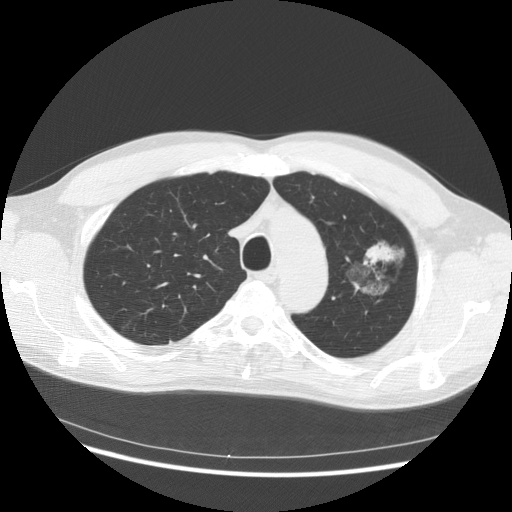
Axial slice from a low-dose chest CT screening exam, third screening round (two years after baseline), lung window (W 1500 / L -600 HU), 2.5 mm slice thickness, slice 109 of 145 in the series, 512 × 512 image matrix. Male, age 61 years at enrolment.
• Lesion marked by an expert reader, box from (x=331, y=236) to (x=406, y=316) px.
• The exam's reader record, not a measurement of the box and not confirmed to be the same lesion: non-calcified nodule or mass ≥4 mm, left upper lobe, 37 × 33 mm, poorly defined margins, mixed attenuation, pre-existing on the prior screen: yes; interval growth: yes.
• Official screen result: positive, other.
• Lung cancer was diagnosed 361 days after this screen: bronchiolo-alveolar adenocarcinoma, NOS, left upper lobe, well differentiated (G1), stage IB (AJCC 6th edition), 44 mm at pathology.